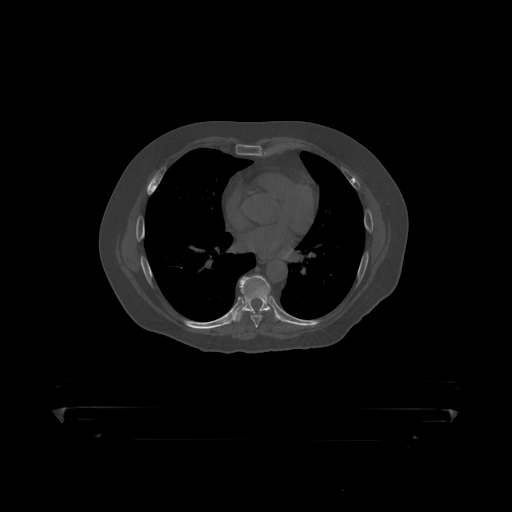
CT including the spine, one axial slice; slice 267 of 390 in the series (ordered by position); reconstruction kernel STANDARD; 120 kVp; bone window (W 1800 / L 400 HU); 512 × 512 image matrix, field of view 650 × 650 mm. Male patient, age 60 years. From the clinical record (not read from this slice): primary cancer: prostate.
Annotated regions visible in this slice (semi-automatic segmentation, software-assisted and operator-edited):
- T7 vertebra: bounding box [x1, y1, x2, y2] px = [247, 311, 267, 319]
- T8 vertebra: [233, 275, 277, 318]